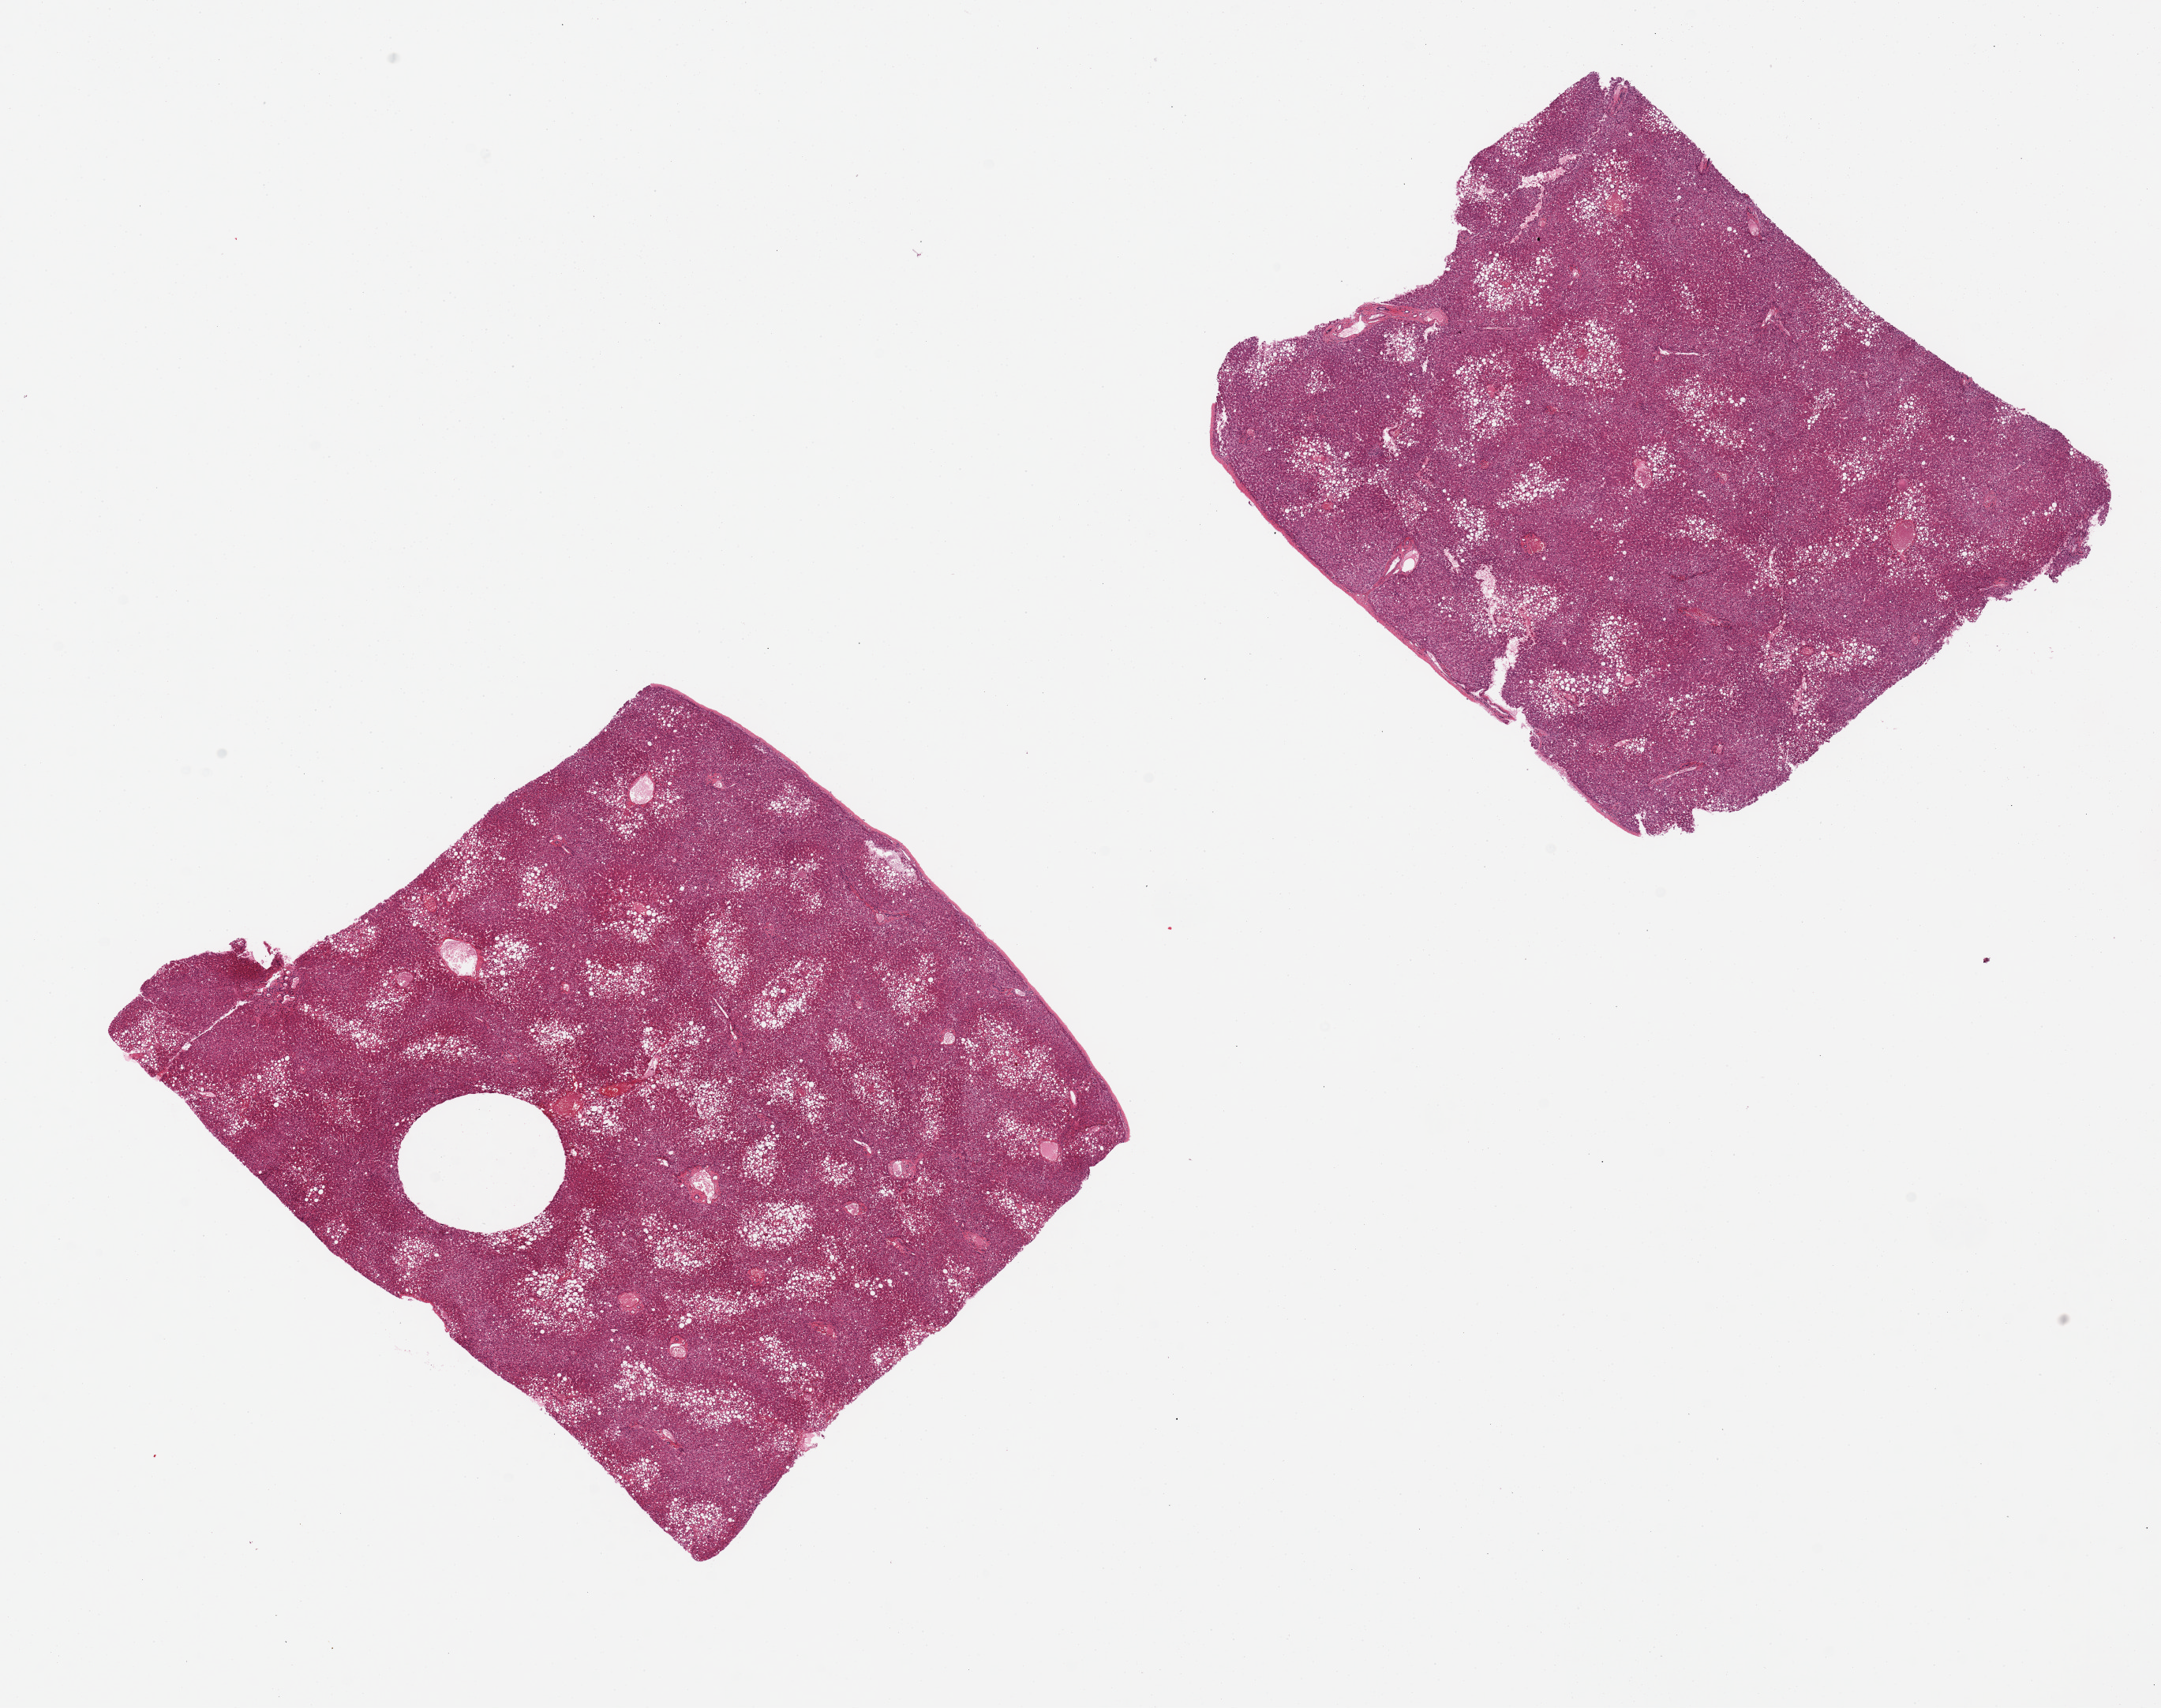
H&E whole-slide image, shown as a low-resolution overview of the whole scanned area (about 21.7 x 17.1 mm), PAXgene-fixed, paraffin-embedded tissue, sampled site (target tissue): liver, tissue donor sample. Female donor.
• pathologist's review note for this sample: 2 pieces, steatosis, sections include capsule (should be 1cm below capsule)